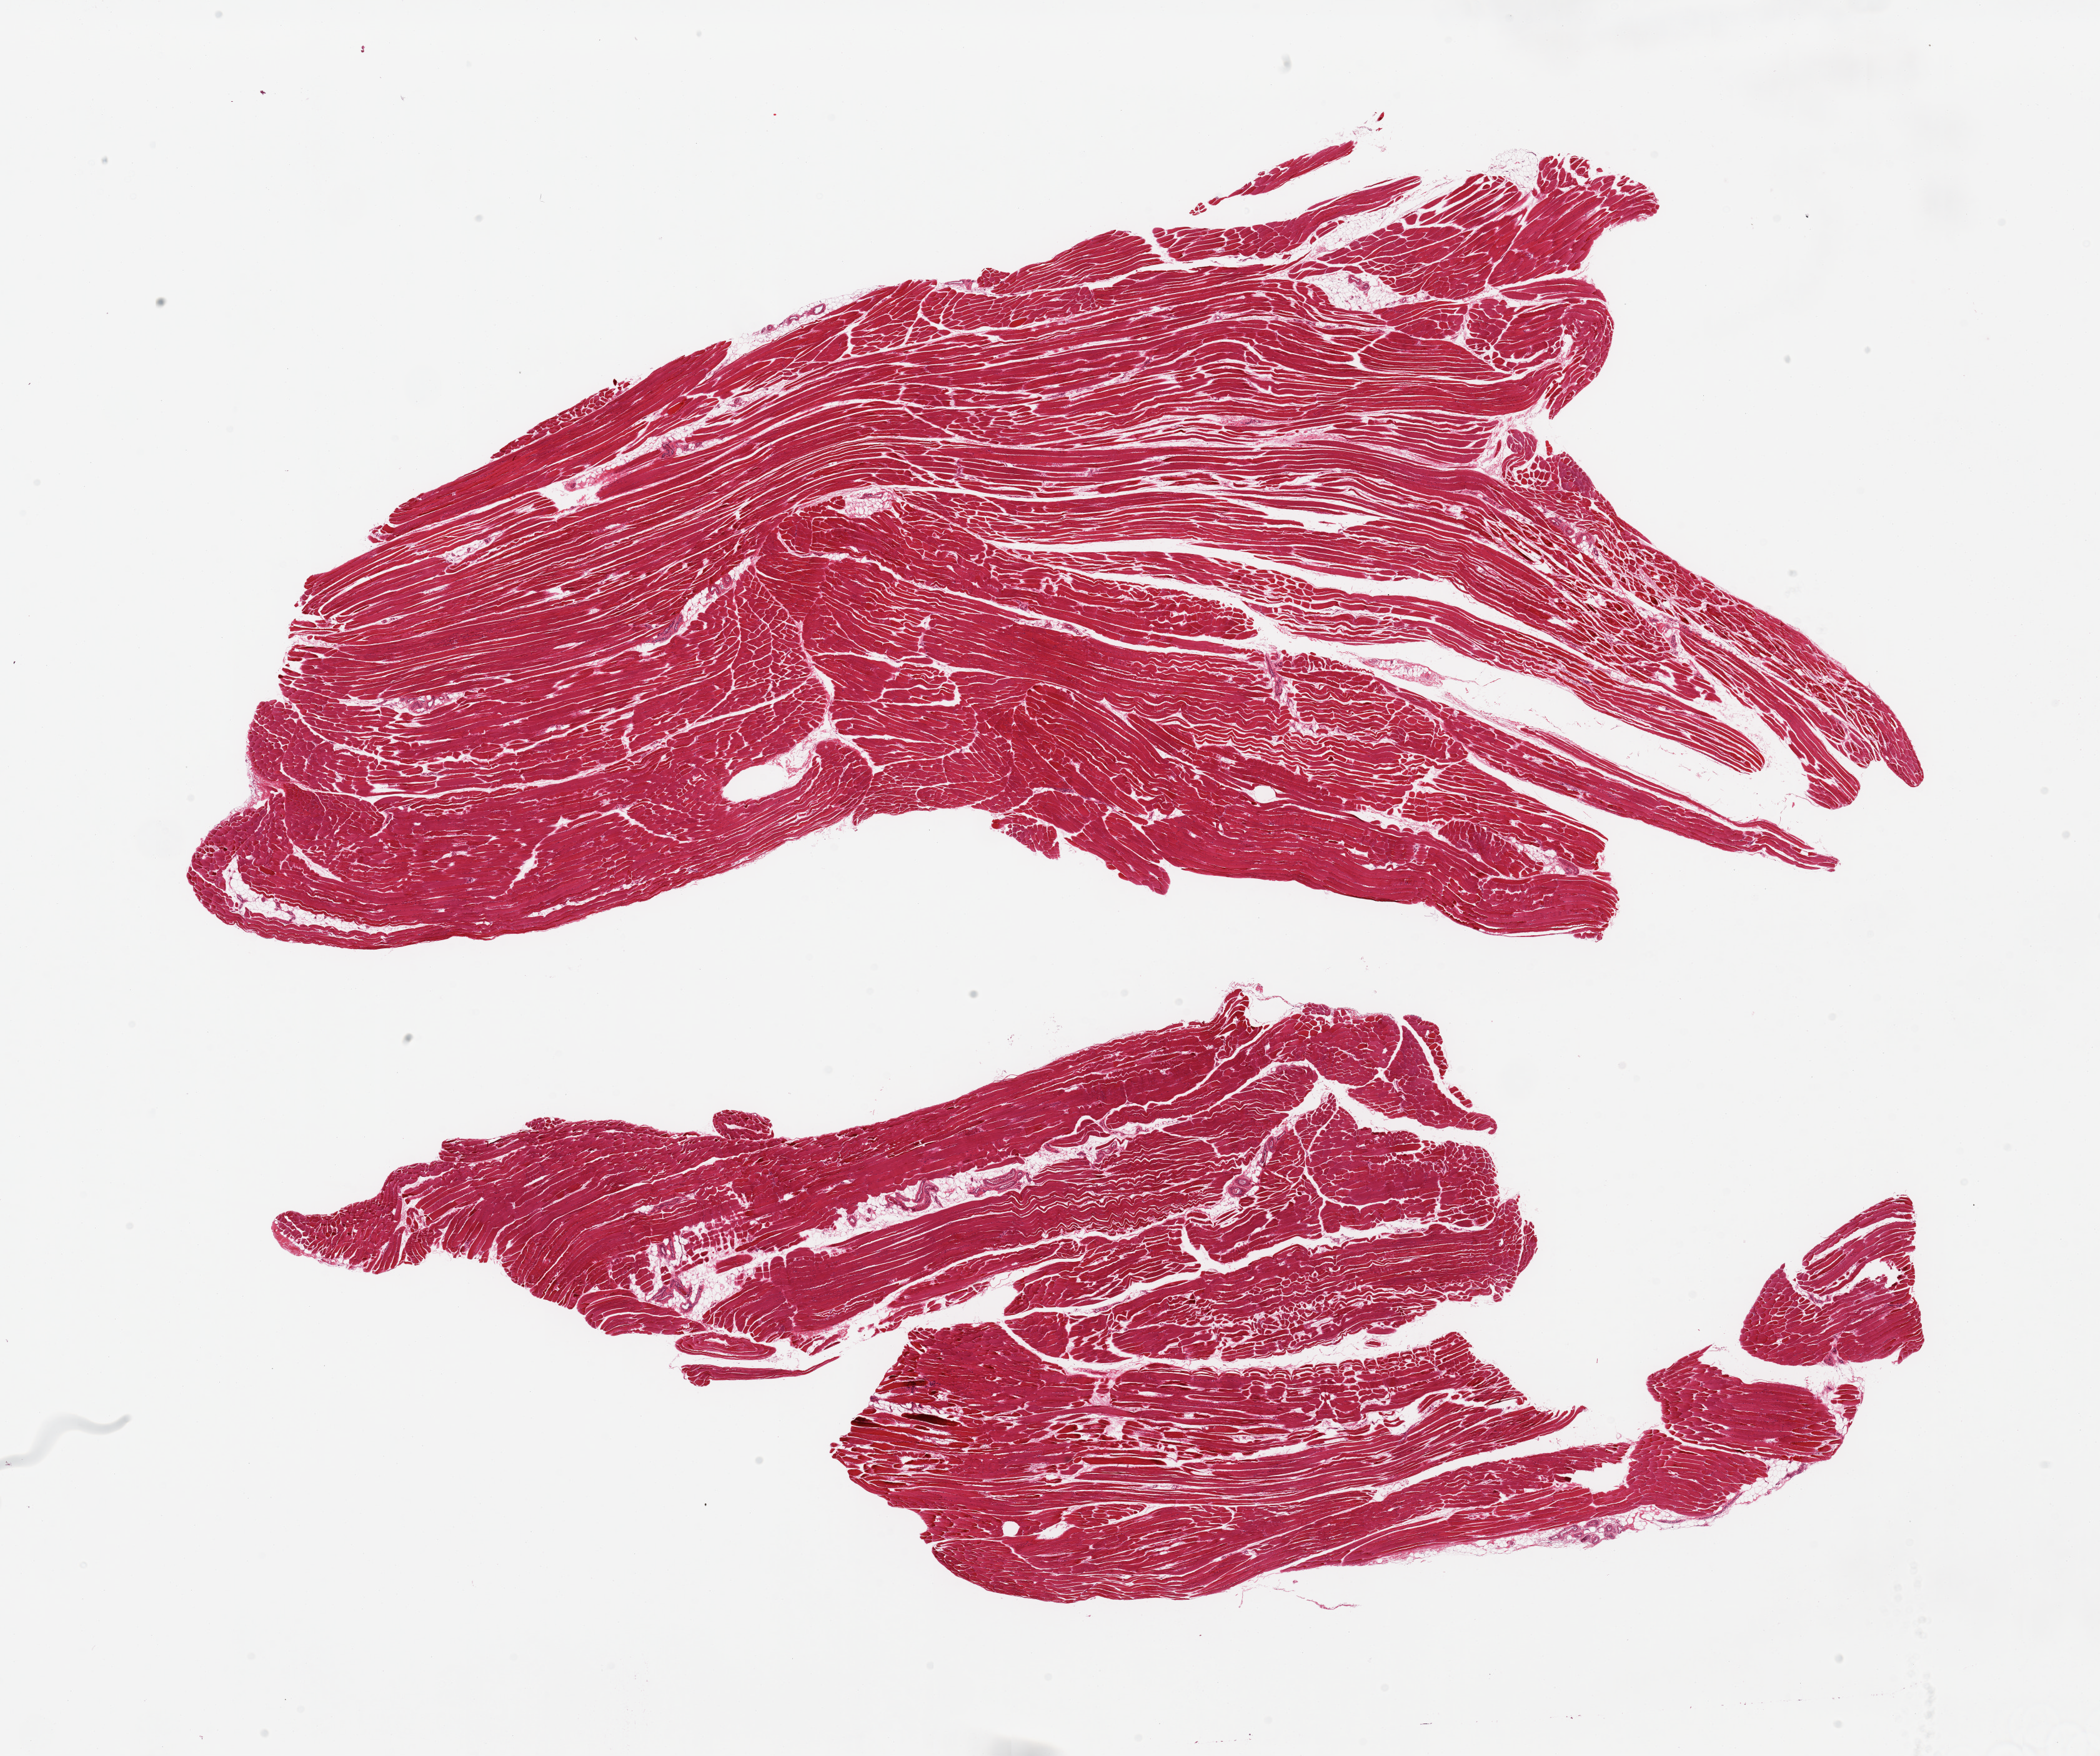
Digitized haematoxylin and eosin-stained section, brightfield — whole scanned area (about 26.6 x 22.2 mm) shown as a low-resolution overview, PAXgene-fixed paraffin-embedded (PFPE) section, section of skeletal muscle (target tissue), tissue donor sample. Donor sex: male.
• reviewer comment on this tissue sample: 2 pieces, ~5-10% interstitial fat, slightly less well preserved than typical